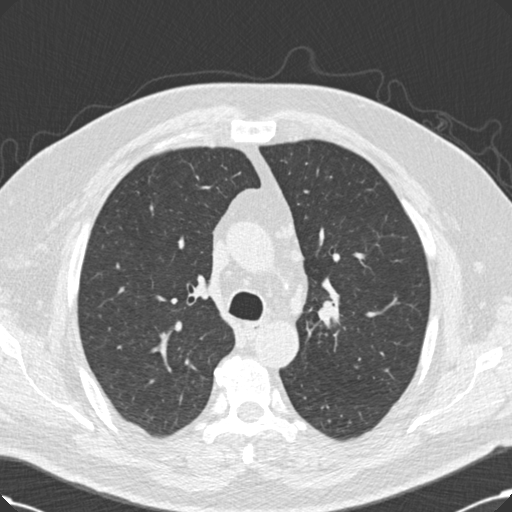
Low-dose screening chest CT, axial slice; third annual screen; lung window (W 1500 / L -600 HU); slice 62 of 214 in the series. Male participant, aged 60 years at enrolment.
• Expert reader's lesion annotation, bounding box <317,293,348,328> (left, top, right, bottom; pixels).
• The exam's reader record, not a measurement of the box and not confirmed to be the same lesion: non-calcified nodule or mass ≥4 mm, left upper lobe, 20 × 20 mm, smooth margins, soft tissue attenuation, pre-existing on the prior screen: no.
• Later outcome: lung cancer diagnosed 53 days after this screen — squamous cell carcinoma, NOS, right upper lobe, 27 mm at pathology.